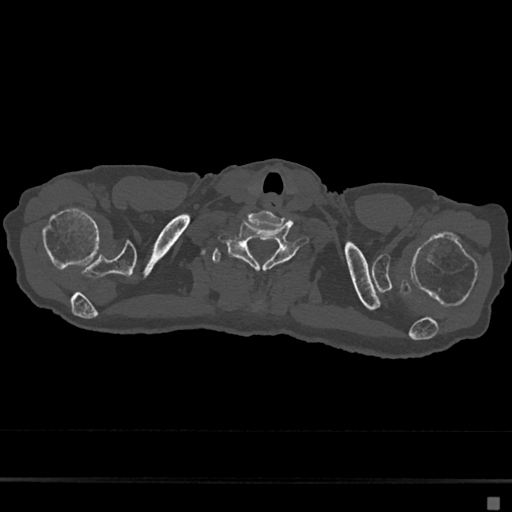
CT including the spine, one axial slice; position 634 of 797 along the scan axis; 120 kVp; bone window (W 1800 / L 400 HU); 512 × 512 image matrix, field of view 360 × 360 mm. Female patient, age 68 years. Case-level facts recorded for this patient, not image findings: primary cancer: renal.
Outlined on this slice (semi-automatic segmentation, software-assisted and operator-edited):
- T1 vertebra: bounding box (x1, y1, x2, y2) in pixels: (212, 249, 263, 306)